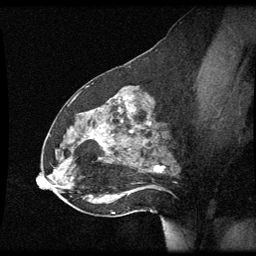
Breast MRI (dynamic contrast-enhanced), one sagittal slice; position 32 of 60 along the scan axis; dynamic contrast-enhanced series, image 2 of 3 at this slice position (ordered by acquisition); 1.5 T; TE 4.2 ms, TR 8.9 ms; 2 mm slice thickness; 256 × 256 image matrix, field of view 200 × 200 mm. Female patient, age 49 years. Case-level facts recorded for this patient, not image findings: setting: breast cancer imaged before/during neoadjuvant chemotherapy; receptor status: HR-positive, HER2-negative.
Annotated regions visible in this slice (semi-automatically segmented with operator editing):
- analysis volume of interest (the breast-tissue region the enhancement analysis was run in; not a lesion): bounding box [x1, y1, x2, y2] px = [46, 92, 177, 205]
- tumour enhancement mask (voxels above the 70 % enhancement threshold inside the analysis volume of interest): [154, 166, 157, 171]